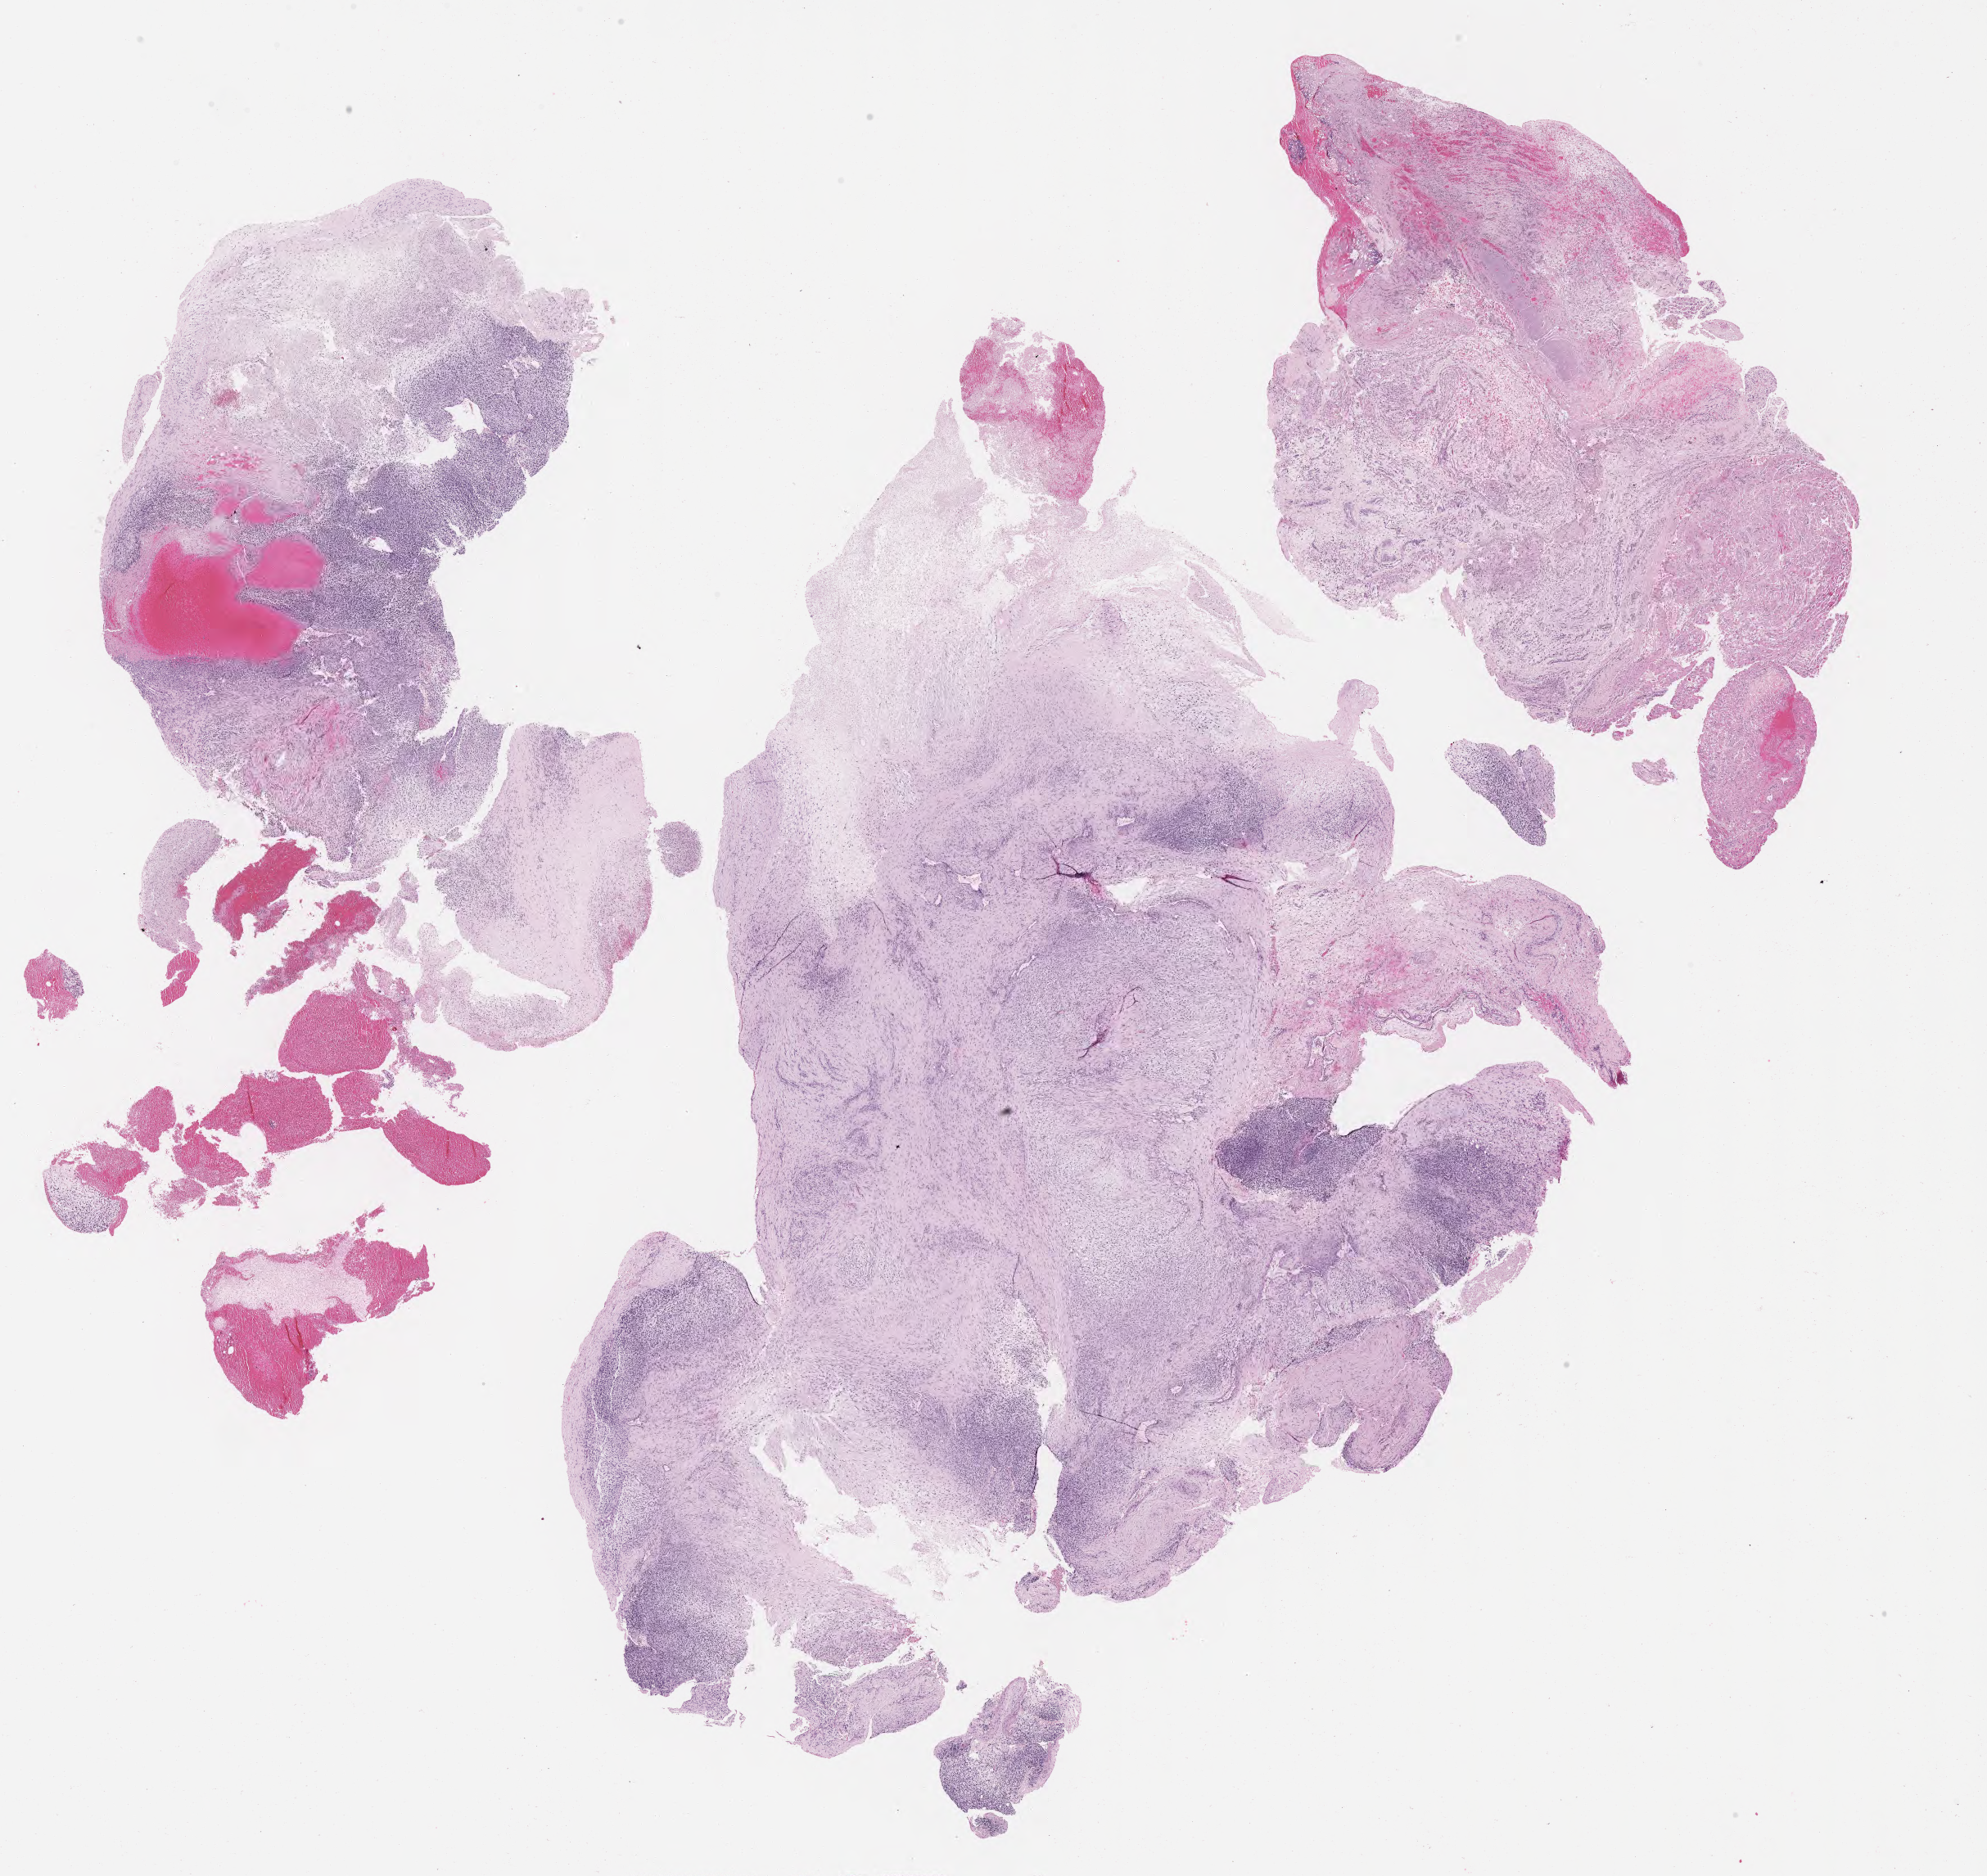
Whole-slide image, hematoxylin and eosin (H&E) stain of tumor tissue, a low-resolution overview of the entire scanned area, about 19.6 x 18.5 mm, formalin-fixed paraffin-embedded section, site: soft tissue - neck, right. Male patient, age at diagnosis 4.9 years.
- metastatic status at presentation (as recorded): metastatic
- stage (as recorded): 4
- diagnosis: rhabdomyosarcoma; histological classification: embryonal rhabdomyosarcoma